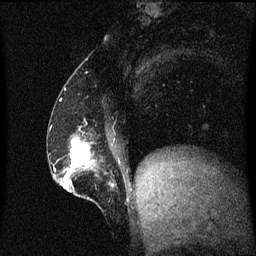
Breast MRI (dynamic contrast-enhanced), one sagittal slice. Position 22 of 60 along the scan axis. Dynamic contrast-enhanced series, image 2 of 3 at this slice position (ordered by acquisition). 1.5 T. TE 4.2 ms, TR 8.4 ms. 2 mm slice thickness. 256 × 256 image matrix, field of view 200 × 200 mm. Female patient, age 52 years. From the clinical record (not read from this slice): setting: breast cancer imaged before/during neoadjuvant chemotherapy; receptor status: HER2-positive.
Outlined on this slice (semi-automatically segmented with operator editing):
- analysis volume of interest (the breast-tissue region the enhancement analysis was run in; not a lesion): bounding box <62,132,116,201> (left, top, right, bottom; pixels)
- tumour enhancement mask (voxels above the 70 % enhancement threshold inside the analysis volume of interest): <66,140,114,191>